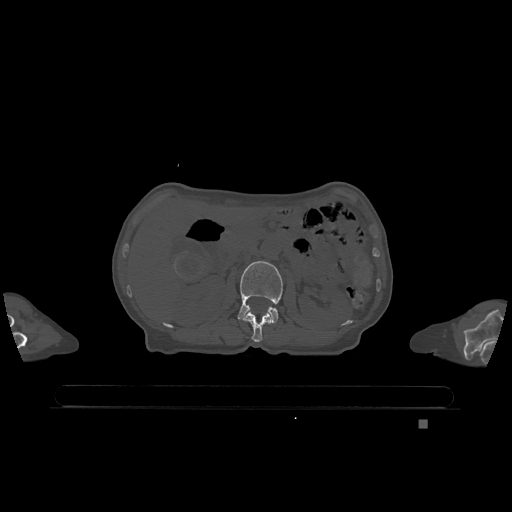
CT including the spine, one axial slice; position 439 of 1317 along the scan axis; bone window (W 1800 / L 400 HU); 0.5 mm slice thickness; 512 × 512 image matrix, field of view 500 × 500 mm. Female patient, age 74 years. From the clinical record (not read from this slice): primary cancer: lung.
Outlined on this slice (semi-automatic segmentation, software-assisted and operator-edited):
- L1 vertebra: bounding box [x1, y1, x2, y2] px = [245, 311, 272, 342]
- L2 vertebra: [238, 261, 283, 324]